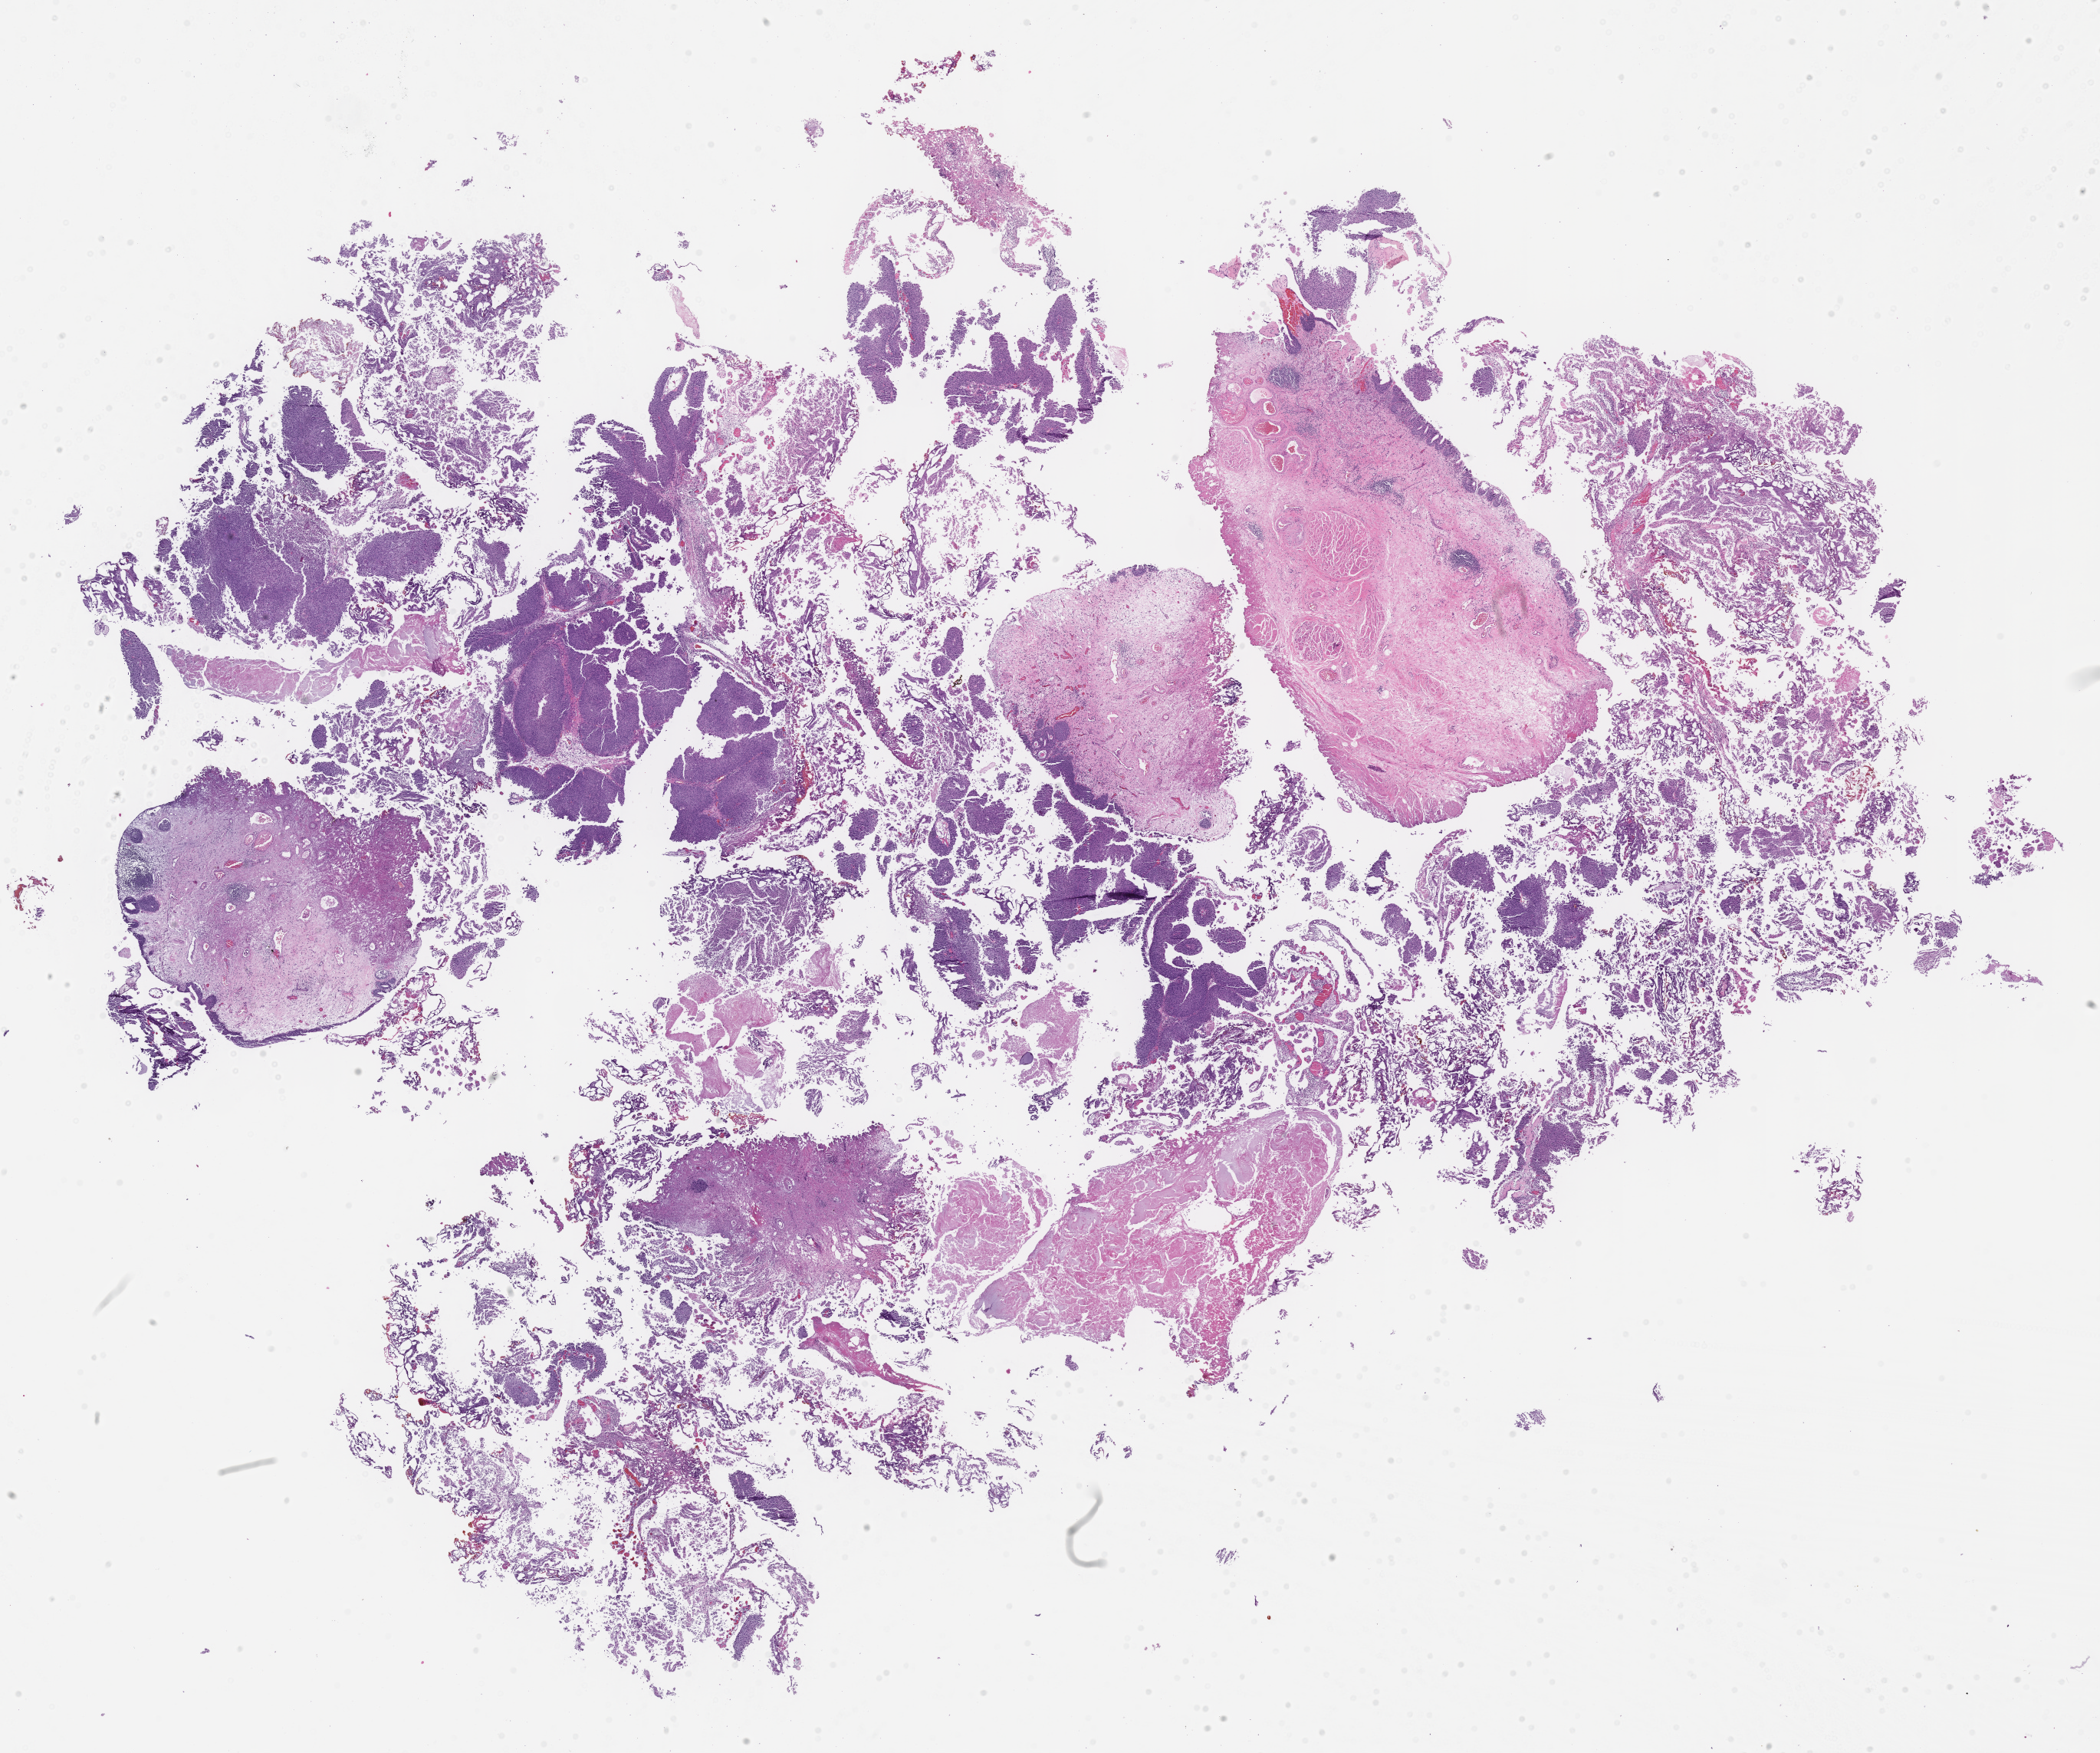
Digitized hematoxylin and eosin (H&E)-stained section — shown as a low-resolution overview of the whole scanned area (about 22.1 x 18.4 mm), formalin-fixed paraffin-embedded section, specimen: primary tumor, site: bladder. Patient: female, age at initial diagnosis 82 years. Slide review estimates, as recorded: tumor cells 35%, tumor nuclei 80%, stromal cells 45%, necrosis 10%, normal cells 10%. Infiltration values recorded for this section: lymphocyte infiltration 0%, monocyte infiltration 0%, neutrophil infiltration 0%.
Section: bottom of the tissue portion. Diagnosis: Papillary urothelial carcinoma, non-invasive.